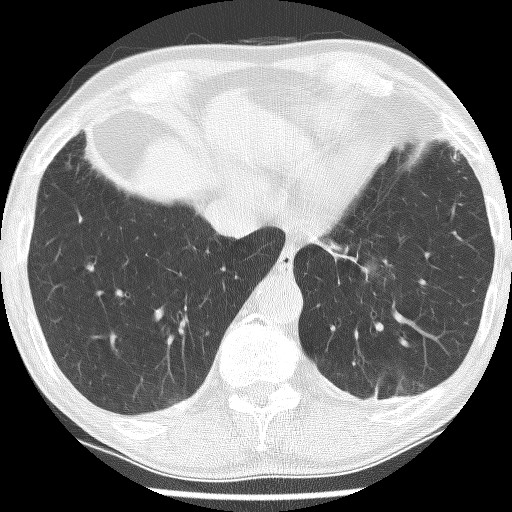
Low-dose screening chest CT, one axial slice. Slice 37 of 226 in the series (ordered by position). Reconstruction kernel BONE. Lung window (W 1500 / L -600 HU). 2.5 mm slice thickness. 512 × 512 image matrix, field of view 320 × 320 mm.
Outlined on this slice (outlined manually by an expert reader):
- lesion 1 (tumor, lower lobe of left lung): box from (x=359, y=261) to (x=378, y=281) px